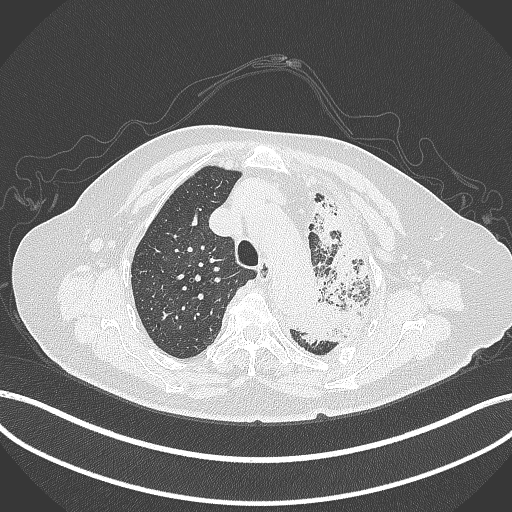
Chest CT, one axial slice. Position 299 of 399 along the scan axis. Reconstruction kernel B70f. 120 kVp. Lung window (W 1500 / L -600 HU). 1 mm slice thickness. 512 × 512 image matrix. Patient: female, 75 years. From the clinical record (not read from this slice): clinical TNM (as recorded): T3 N3 M1.
Annotated regions visible in this slice (rectangle marked by the reading radiologist):
- lung tumour (recorded histology: adenocarcinoma): bounding box (x1, y1, x2, y2) in pixels: (294, 197, 370, 353)